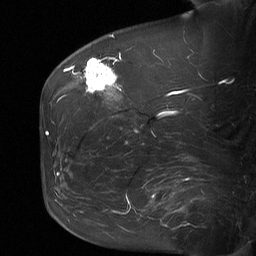
Breast MRI (dynamic contrast-enhanced), one sagittal slice. Position 22 of 64 along the scan axis. Dynamic contrast-enhanced study with each time point stored as its own series, time point 2 of 3 at this slice position (early post-contrast, ordered by acquisition time). 1.5 T. TE 4.8 ms, TR 27 ms. 2 mm slice thickness. 256 × 256 image matrix, field of view 200 × 200 mm. Female patient, age 60 years. From the clinical record (not read from this slice): setting: breast cancer imaged before/during neoadjuvant chemotherapy; receptor status: HR-positive, HER2-negative.
Outlined on this slice (semi-automatically segmented with operator editing):
- analysis volume of interest (the breast-tissue region the enhancement analysis was run in; not a lesion): bounding box (x1, y1, x2, y2) in pixels: (79, 50, 122, 99)
- tumour enhancement mask (voxels above the 90 % enhancement threshold inside the analysis volume of interest): (85, 58, 117, 92)